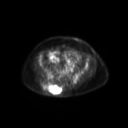
FDG PET of an extremity soft-tissue mass (from a PET/CT study), one axial slice. Position 74 of 267 along the scan axis. 3.27 mm slice thickness. 128 × 128 image matrix, field of view 600 × 600 mm. Patient: female, 60 years. From the clinical record (not read from this slice): histological type: spindle cell suggestive of myxofibrosarcoma; grade: intermediate; site of the primary tumour: right buttock.
Structures marked on this image (expert contour drawn on MRI and transferred to this co-registered scan by the dataset authors):
- gross tumour volume (mass): box from (x=41, y=85) to (x=63, y=95) px